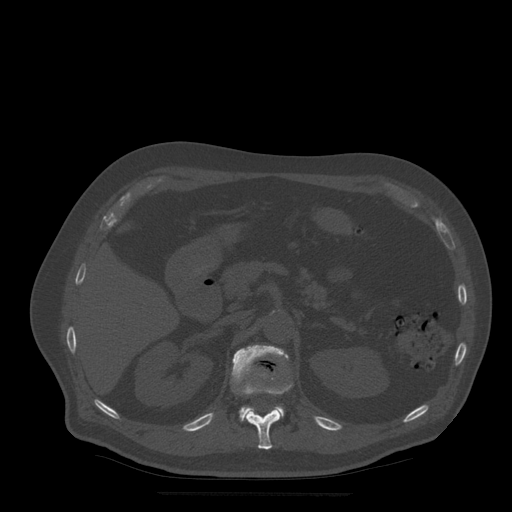
CT including the spine, one axial slice. Slice 210 of 522 in the series (ordered by position). Bone window (W 1800 / L 400 HU). 1.25 mm slice thickness. 512 × 512 image matrix, field of view 420 × 420 mm. Patient age 72 years. From the clinical record (not read from this slice): primary cancer: prostate.
Outlined on this slice (semi-automatic segmentation, software-assisted and operator-edited):
- L1 vertebra: bounding box [x1, y1, x2, y2] px = [232, 345, 289, 421]
- T12 vertebra: [246, 377, 292, 450]